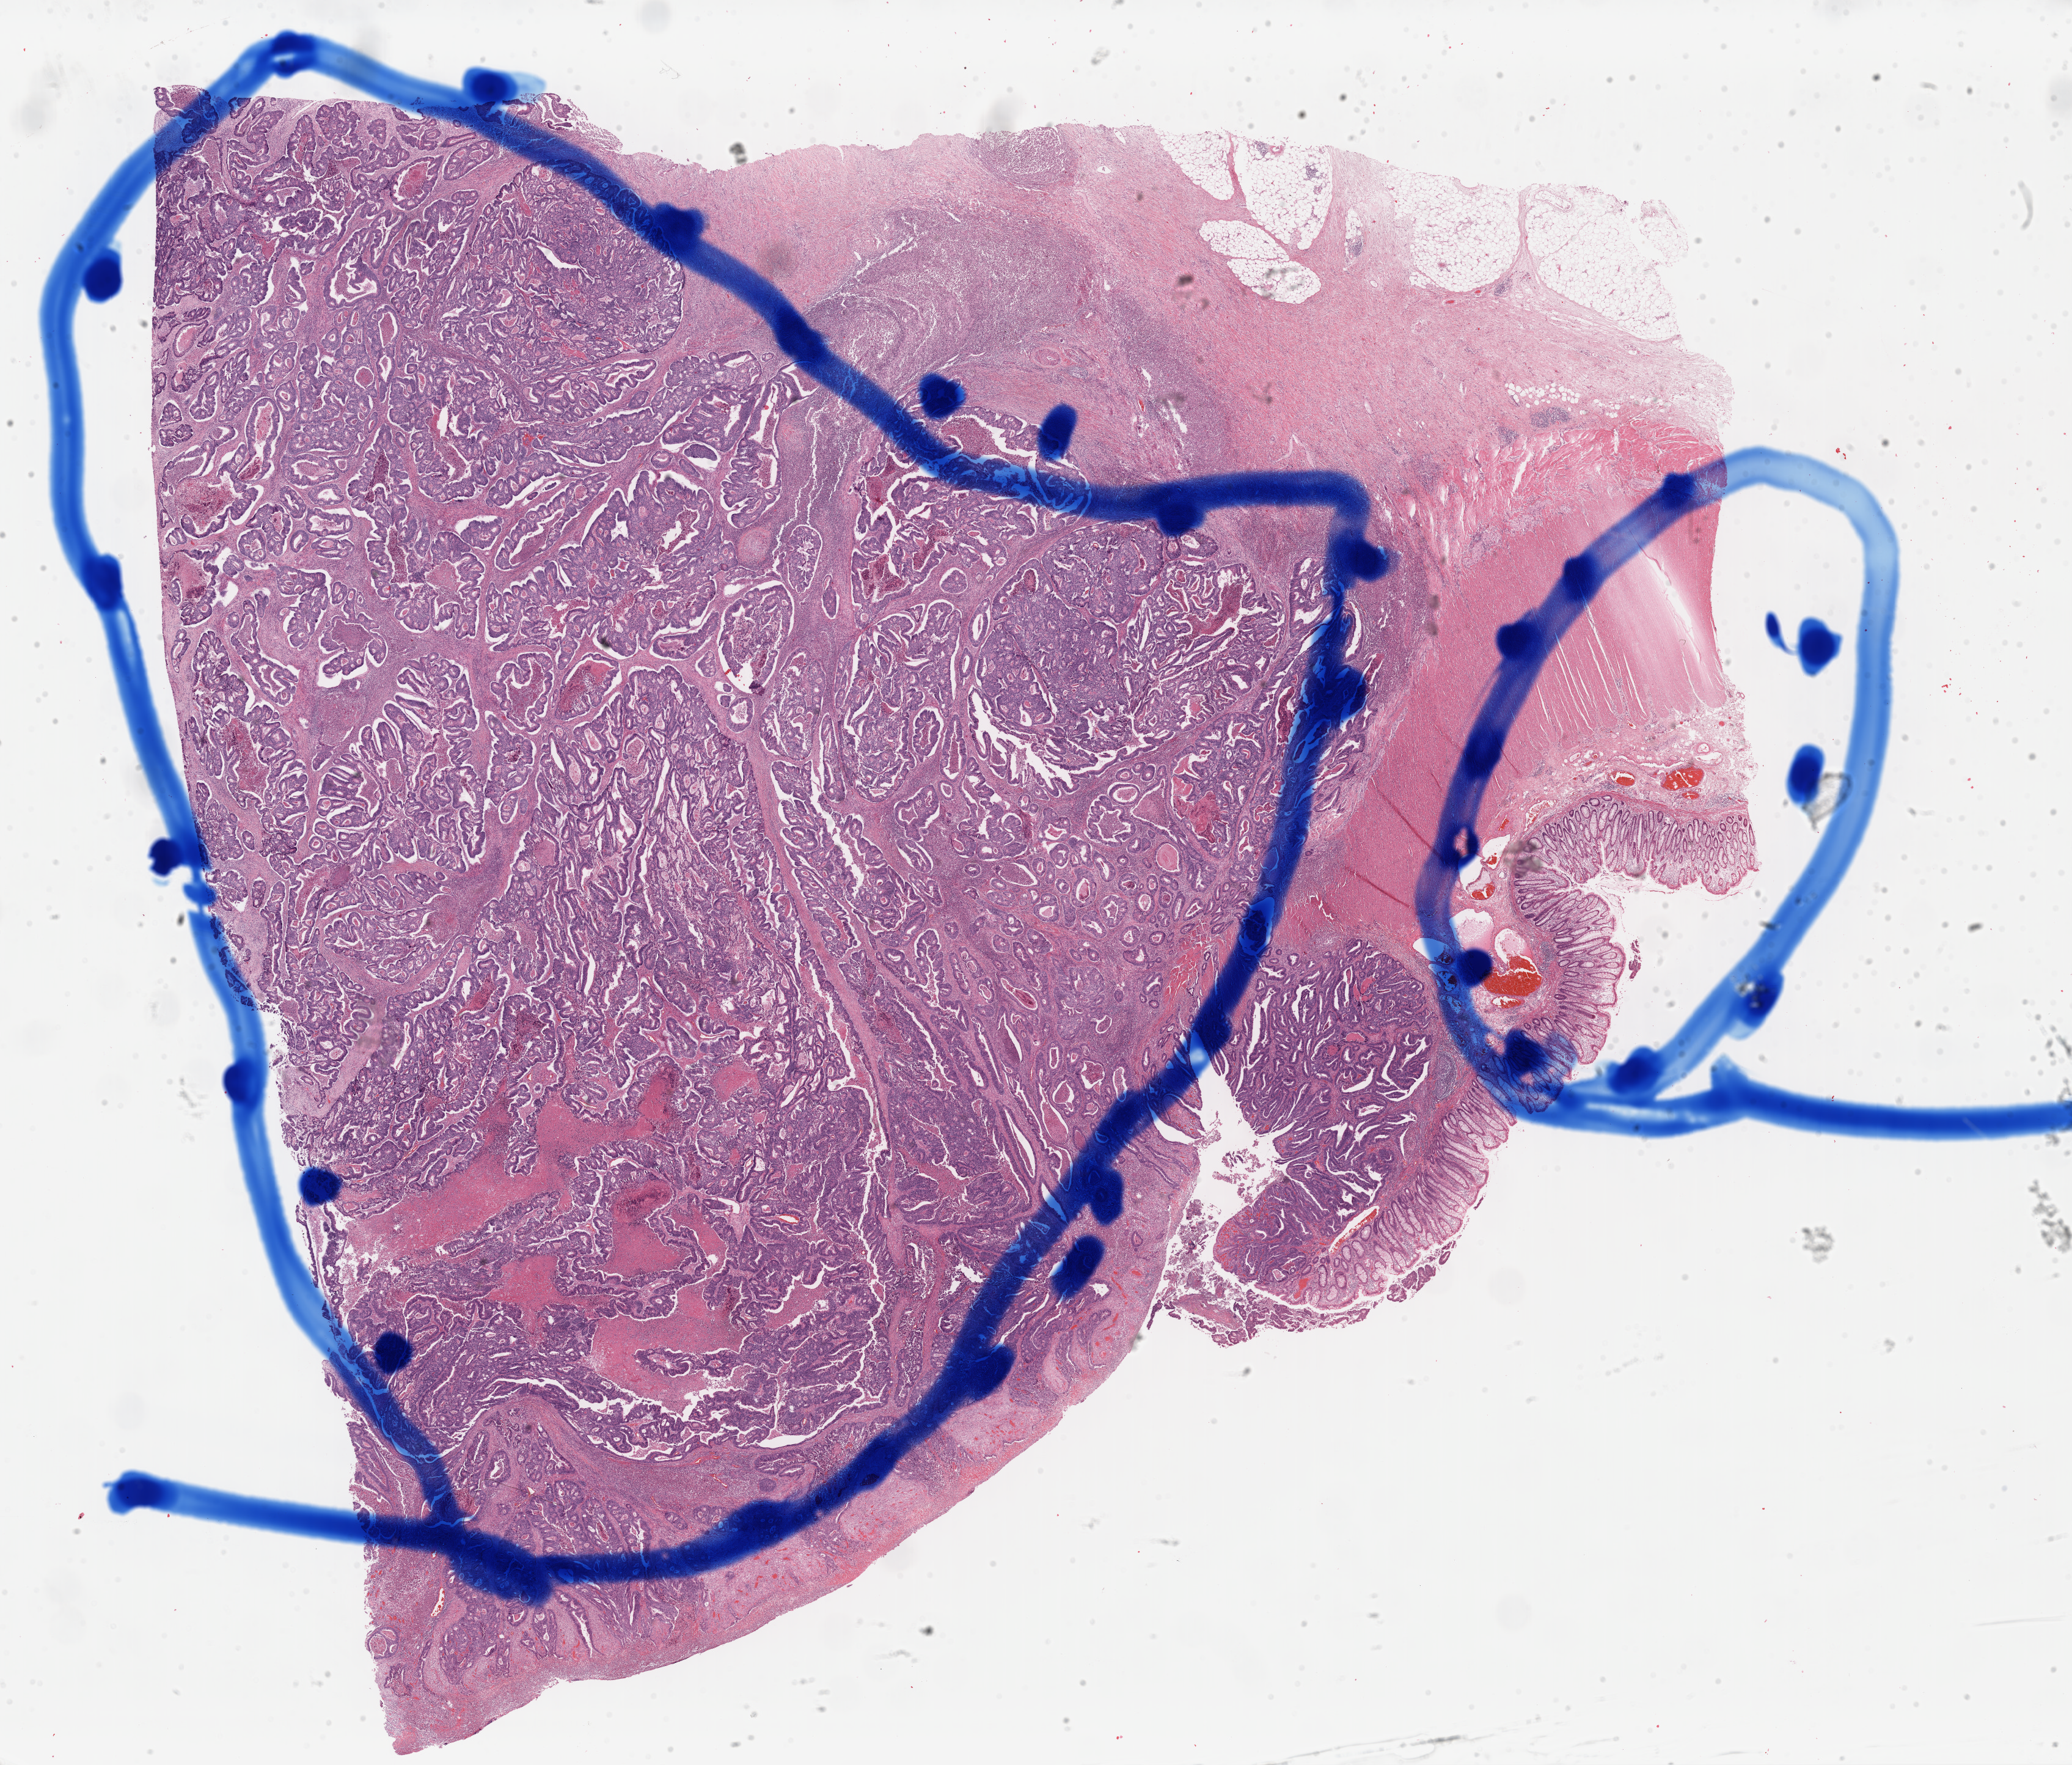
H&E-stained whole-slide image — shown as a low-resolution overview of the whole scanned area (about 26.8 x 22.8 mm, from a 40x scan); FFPE section; sample: primary tumour, rectum. Female patient; age at initial diagnosis 57 years.
• lymph nodes positive (case pathology): 0 of 14 examined
• histologic diagnosis: Adenocarcinoma, NOS
• AJCC pathologic stage: IIA